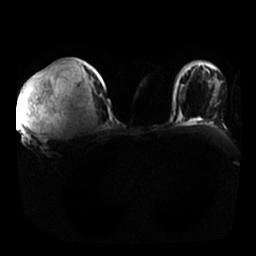
Breast MRI, one axial slice. Slice 16 of 25 in the series (ordered by position). Diffusion-weighted series; image 2 of 4 stored at this slice position (different b-values; order by instance number). 1.5 T. 256 × 256 image matrix, field of view 350 × 350 mm. Female patient.
Outlined on this slice (outlined manually by an expert reader):
- tumour on diffusion-weighted imaging: bounding box [x1, y1, x2, y2] px = [20, 78, 43, 133]